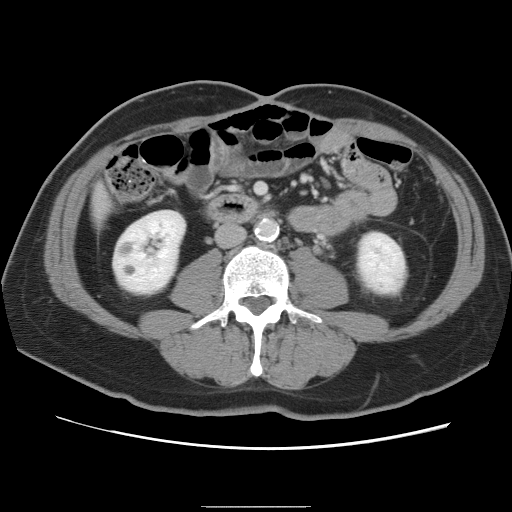
Contrast-enhanced abdominal CT, one axial slice; slice 16 of 87 in the series (ordered by position); 120 kVp; intravenous contrast given; soft-tissue window (W 400 / L 40 HU); 5 mm slice thickness; 512 × 512 image matrix, field of view 363 × 363 mm. Male patient, age 63 years. From the clinical record (not read from this slice): diagnosis: colorectal cancer liver metastases, imaged before liver resection; multiple liver metastases: no; largest metastasis: 9 cm; disease in both lobes: no.
Outlined on this slice (expert manual segmentation):
- liver: bounding box [x1, y1, x2, y2] px = [93, 189, 110, 216]
- planned liver remnant (the part of the liver to remain after resection): [92, 188, 110, 216]